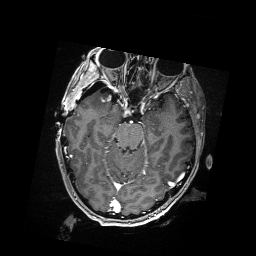
Brain MRI from a brain-tumour surgery series, one axial slice; position 113 of 176 along the scan axis; T1-weighted post-contrast; 1 mm slice thickness; 256 × 256 image matrix, field of view 256 × 256 mm. From the clinical record (not read from this slice): histopathology: Metastatic Carcinoma from Breast primary; tumour location: Right Frontal.
Outlined on this slice (manually delineated by an expert):
- residual tumour: bounding box (x1, y1, x2, y2) in pixels: (91, 88, 102, 95)